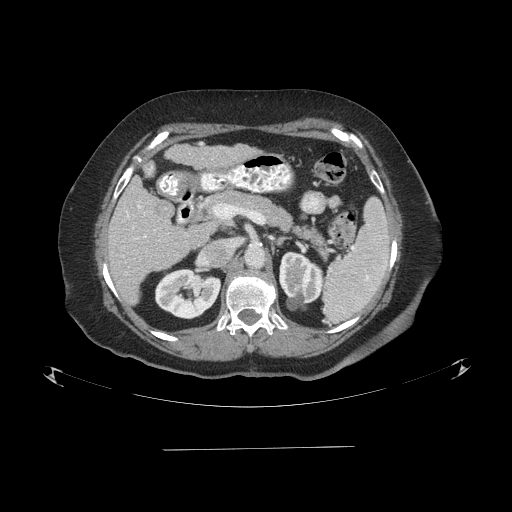
Contrast-enhanced abdominal CT (liver protocol), one axial slice; slice 43 of 103 in the series (ordered by position); reconstruction kernel STANDARD; 120 kVp; one of 2 acquisitions stored at this slice position; soft-tissue window (W 400 / L 40 HU); 2.5 mm slice thickness; 512 × 512 image matrix, field of view 500 × 500 mm. From the clinical record (not read from this slice): diagnosis: hepatocellular carcinoma (patient treated with transarterial chemoembolisation; whether this scan precedes or follows treatment is not stated here); TNM stage (as recorded): Stage-IIIA; Child-Pugh class: A; tumour nodularity: multinodular; tumour size: 5.2 cm.
Annotated regions visible in this slice (semi-automatic segmentation, software-assisted and operator-edited):
- liver parenchyma outside the tumour (the mass and vessels are separate outlines, so this box may not span the whole liver): bounding box <106,176,214,304> (left, top, right, bottom; pixels)
- liver vessels: <127,205,146,237>